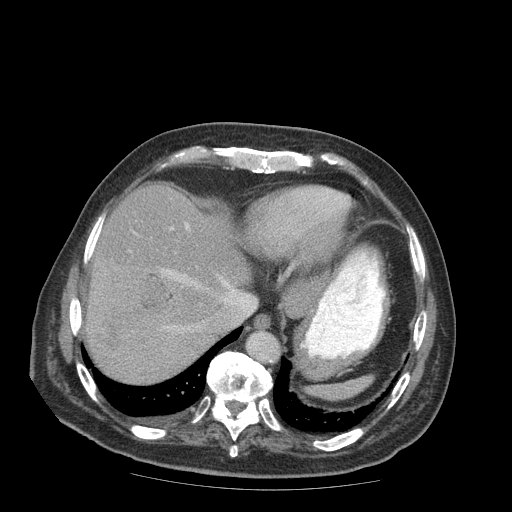
Contrast-enhanced abdominal CT (liver protocol), one axial slice. Position 73 of 99 along the scan axis. 140 kVp. Soft-tissue window (W 400 / L 40 HU). 2.5 mm slice thickness. 512 × 512 image matrix, field of view 420 × 420 mm. Case-level facts recorded for this patient, not image findings: diagnosis: hepatocellular carcinoma (patient treated with transarterial chemoembolisation; whether this scan precedes or follows treatment is not stated here); TNM stage (as recorded): Stage-IIIB; Child-Pugh class: A; tumour differentiation: well differentiated.
Structures marked on this image (semi-automatically segmented with operator editing):
- liver parenchyma outside the tumour (the mass and vessels are separate outlines, so this box may not span the whole liver): bounding box (x1, y1, x2, y2) in pixels: (86, 184, 248, 382)
- mass: (85, 255, 172, 344)
- liver vessels: (134, 223, 237, 332)